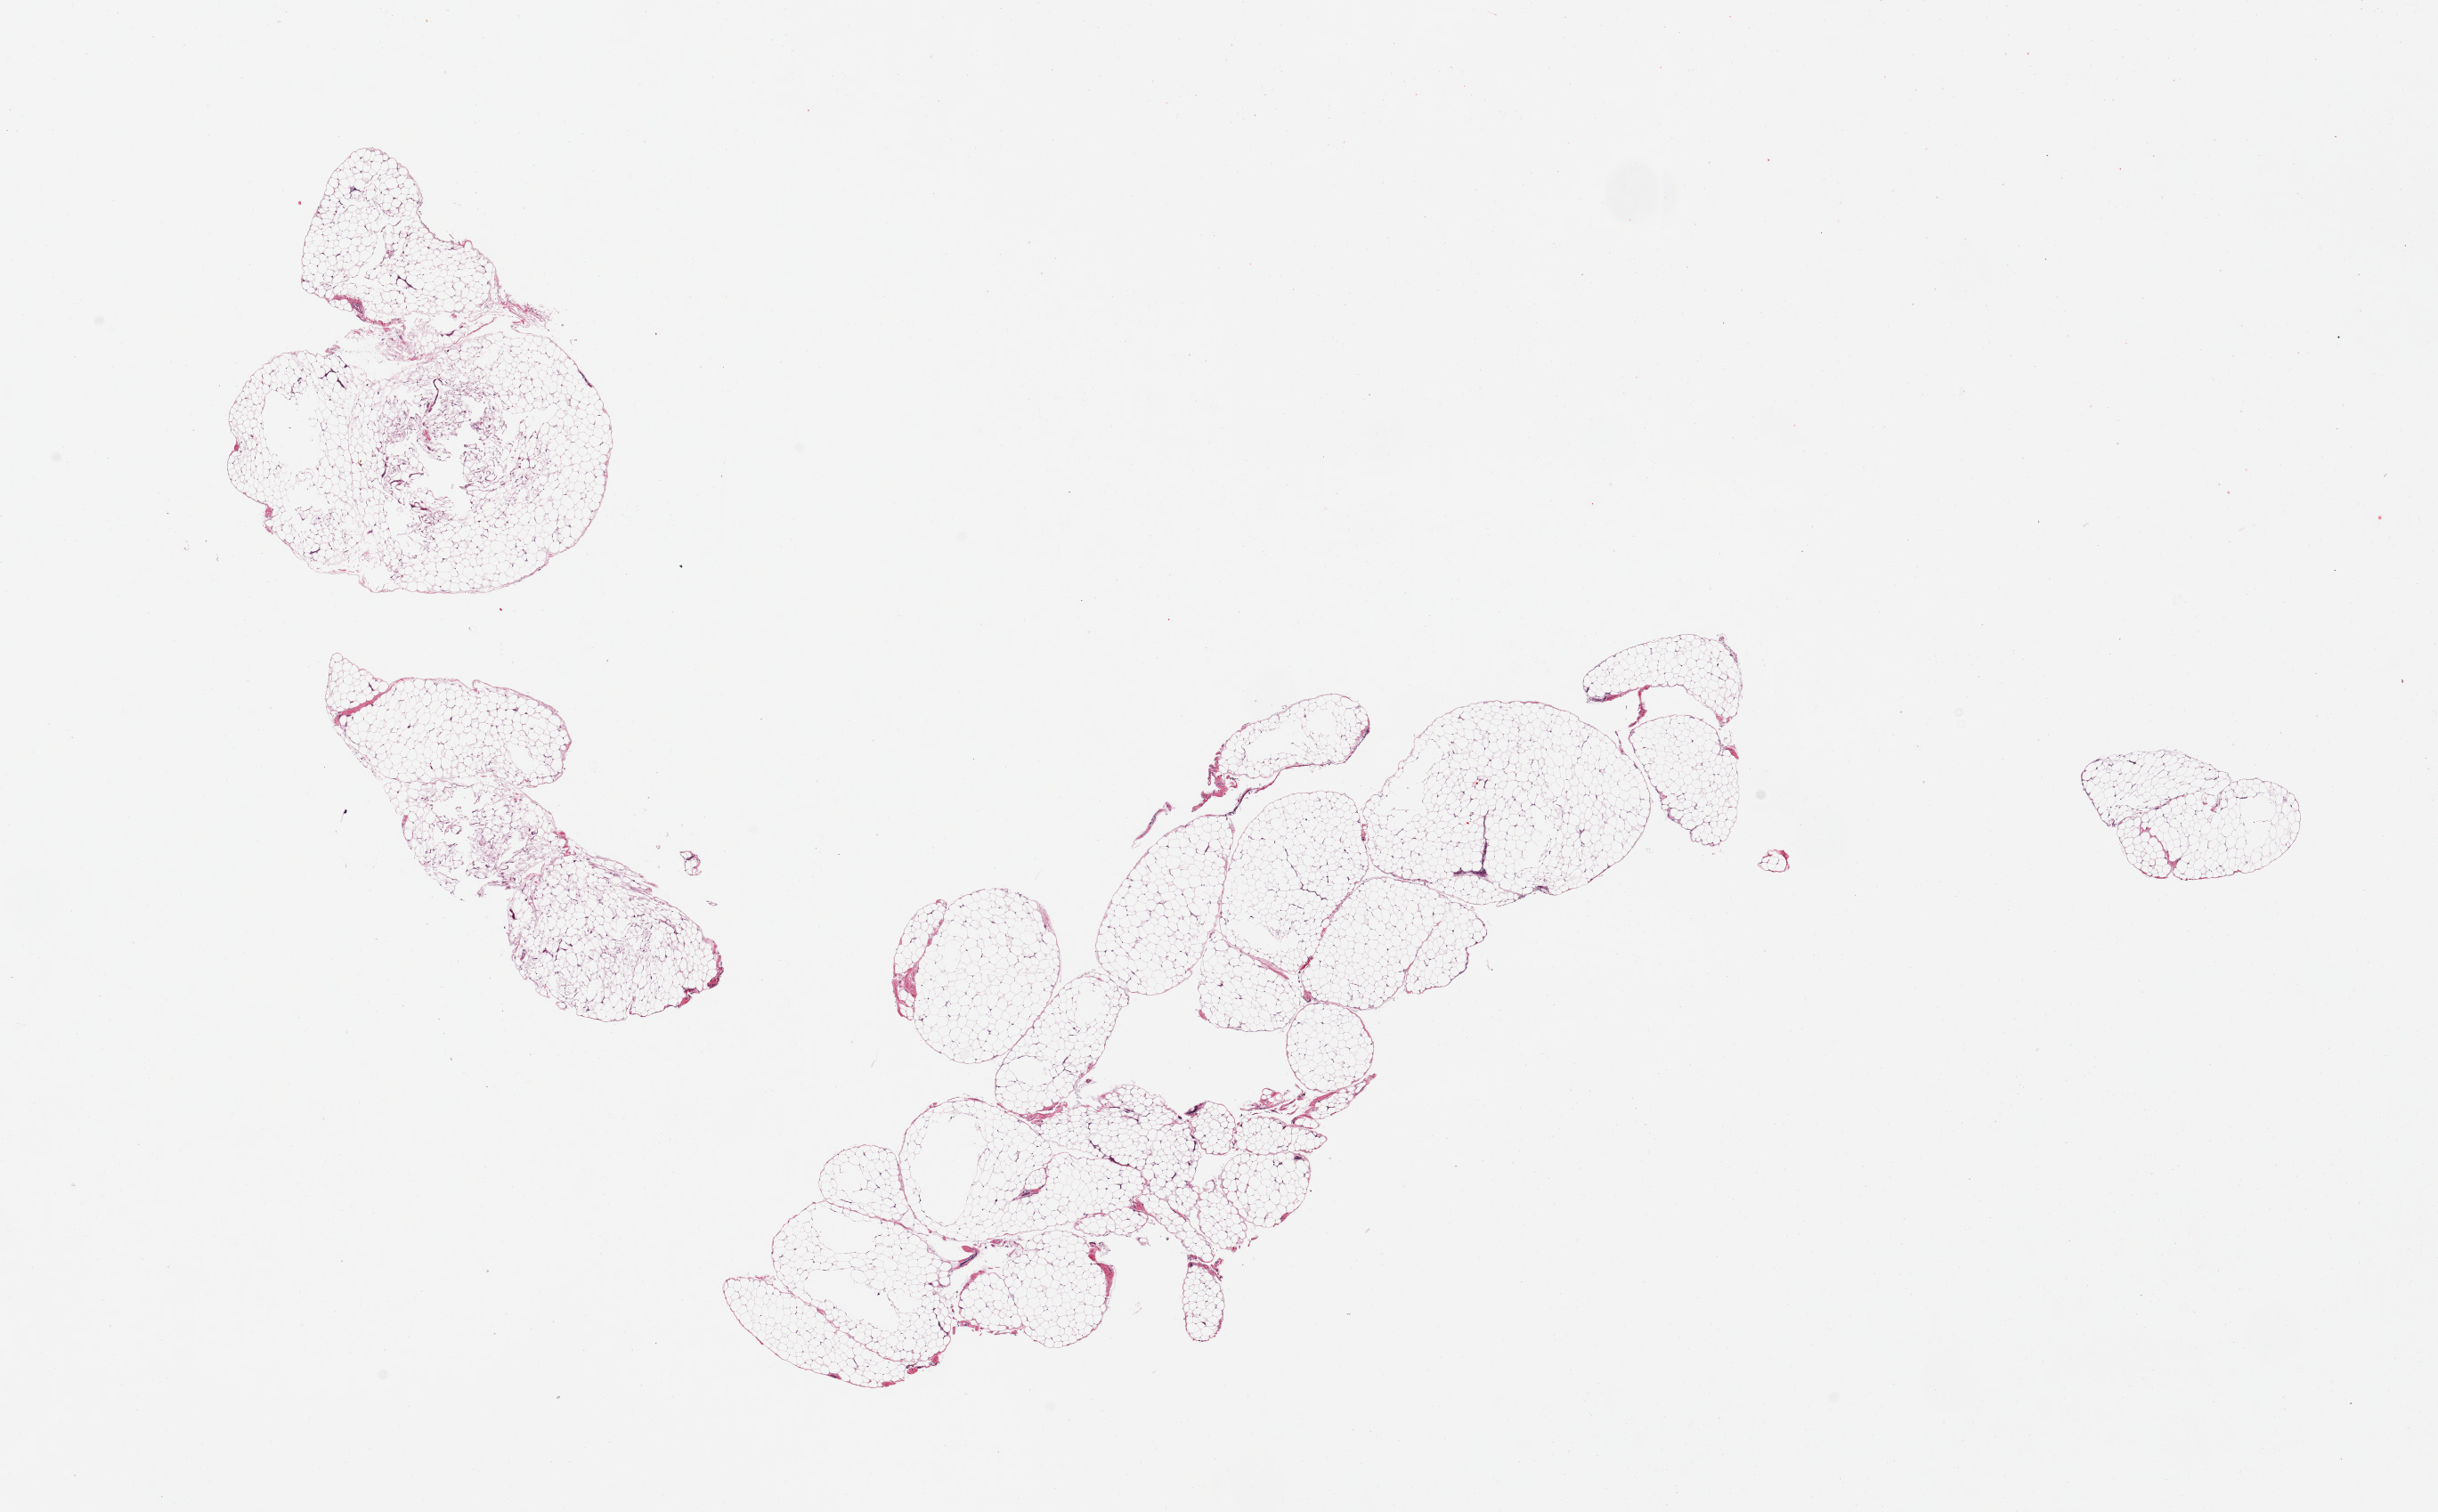
Hematoxylin and eosin (H&E) whole-slide image — shown as a low-resolution overview of the whole scanned area (about 21.7 x 13.4 mm). PAXgene-fixed paraffin-embedded (PFPE) section. Section of omentum (target tissue). Tissue donor sample. Female donor.
Pathologist's review note for this sample: 2 pieces, fragmented; mature adipose tissue.